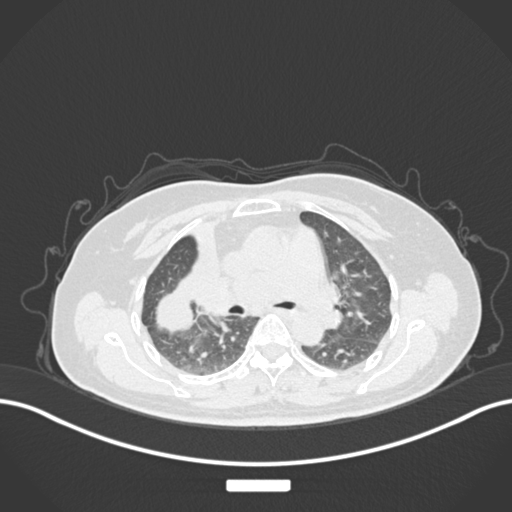
Chest CT, one axial slice; slice 94 of 177 in the series (ordered by position); reconstruction kernel B30f; lung window (W 1500 / L -600 HU); 1 mm slice thickness; 512 × 512 image matrix. Patient: female, 60 years. Case-level facts recorded for this patient, not image findings: clinical TNM (as recorded): T3 N1 M1.
Outlined on this slice (bounding box drawn by a radiologist):
- lung tumour (recorded histology: adenocarcinoma): bounding box (x1, y1, x2, y2) in pixels: (143, 278, 204, 339)